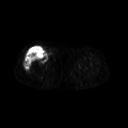
FDG PET of an extremity soft-tissue mass (from a PET/CT study), one axial slice; position 237 of 311 along the scan axis; 3.27 mm slice thickness; 128 × 128 image matrix, field of view 500 × 500 mm. Patient: female, 57 years. From the clinical record (not read from this slice): histological type: pleiomorphic undifferentiated sarcoma; grade: high; site of the primary tumour: right quadricep.
Outlined on this slice (expert contour drawn on MRI and transferred to this co-registered scan by the dataset authors):
- tumour plus oedema (research contour): bounding box [x1, y1, x2, y2] px = [25, 48, 46, 70]
- tumour (research contour): [25, 48, 46, 70]